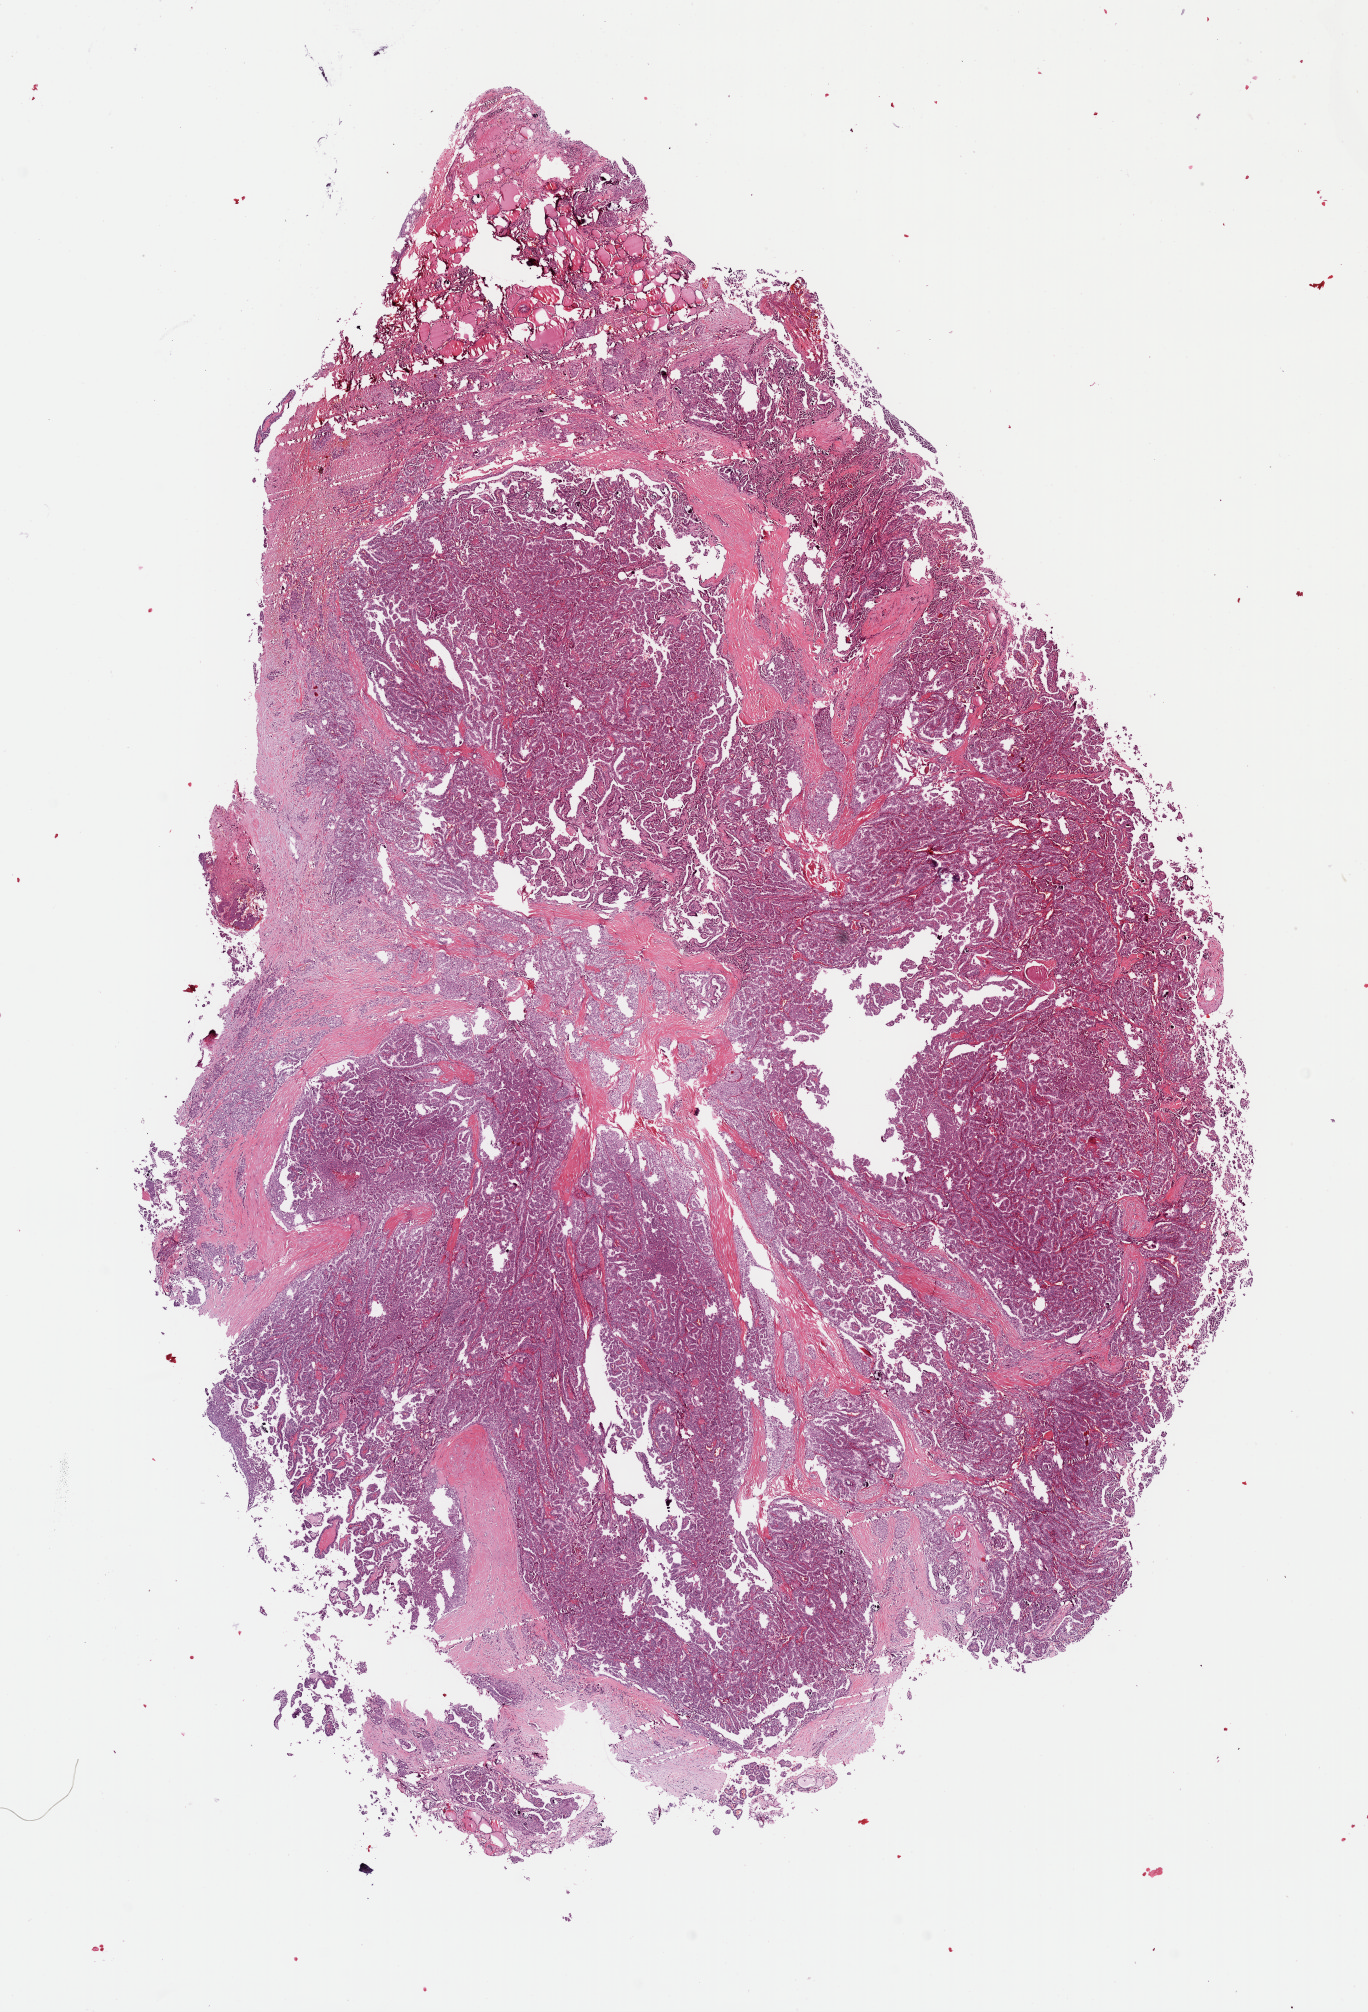
Hematoxylin and eosin (H&E) stained whole-slide image, shown as a low-resolution overview of the whole scanned area (about 10.8 x 15.9 mm). Formalin-fixed paraffin-embedded (FFPE) diagnostic section. Sample: primary tumour, thyroid. Male, age 32 years at initial diagnosis.
Histologic diagnosis: Papillary adenocarcinoma, NOS (thyroid gland).